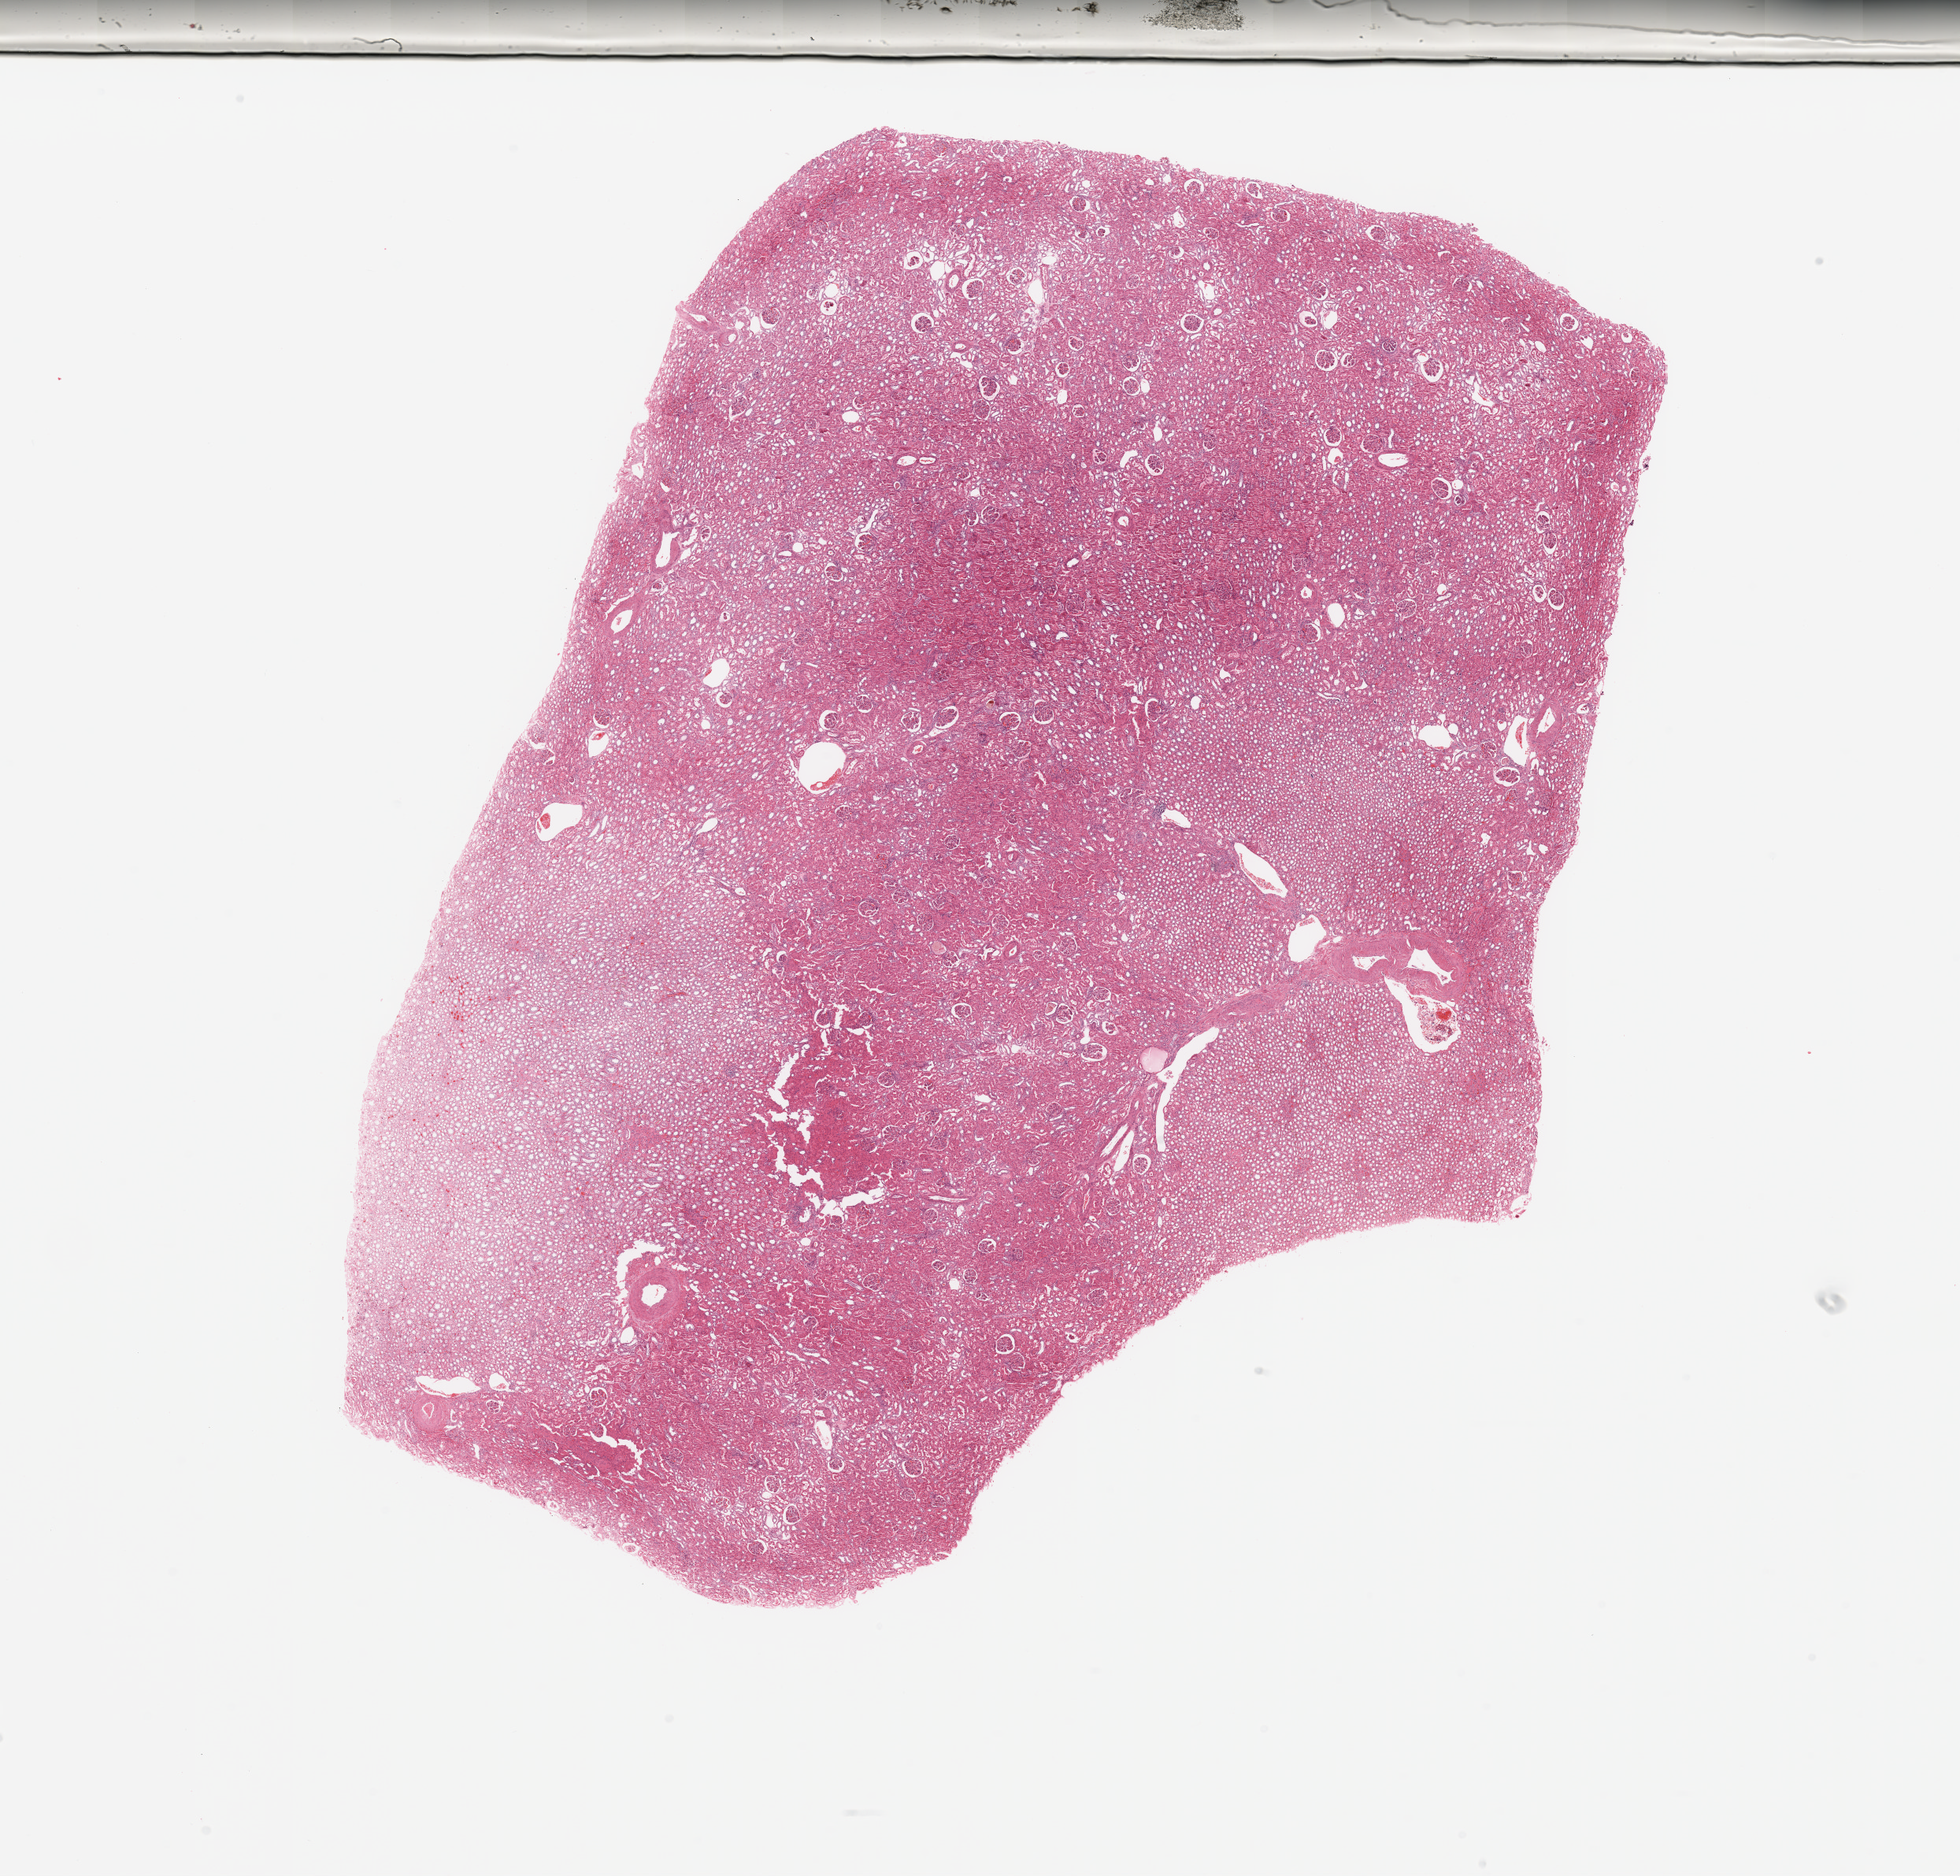
H&E-stained whole-slide image — whole scanned area (about 19.7 x 18.8 mm, from a 20x scan) shown as a low-resolution overview, normal (non-tumour) tissue sample, kidney. Patient: male, age 52 years.
* this section: normal (non-tumour) tissue from the same patient
* patient diagnosis: Renal cell carcinoma, NOS